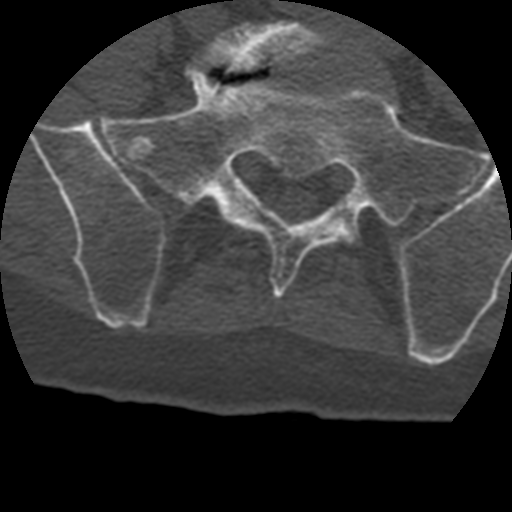
CT including the spine, one axial slice; 120 kVp; bone window (W 1800 / L 400 HU); 512 × 512 image matrix. Patient age 69 years. From the clinical record (not read from this slice): primary cancer: prostate.
Annotated regions visible in this slice (semi-automatically segmented with operator editing):
- L5 vertebra: bounding box [x1, y1, x2, y2] px = [195, 20, 334, 72]